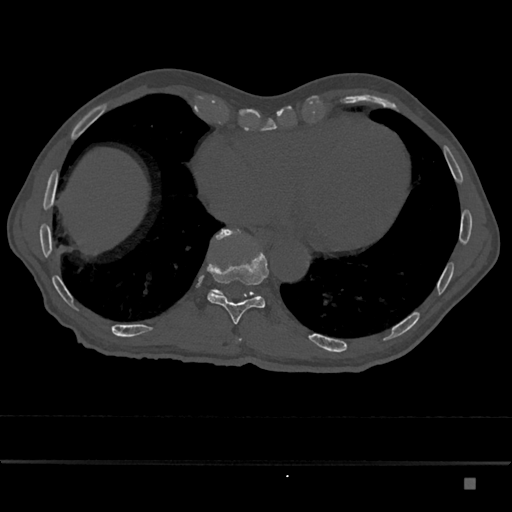
CT including the spine, one axial slice; bone window (W 1800 / L 400 HU); 0.5 mm slice thickness; 512 × 512 image matrix, field of view 390 × 390 mm. Male patient, age 72 years. From the clinical record (not read from this slice): primary cancer: prostate.
Structures marked on this image (semi-automatic segmentation, software-assisted and operator-edited):
- T10 vertebra: bounding box <207,234,269,324> (left, top, right, bottom; pixels)
- T11 vertebra: <209,229,256,297>
- T9 vertebra: <238,339,242,341>